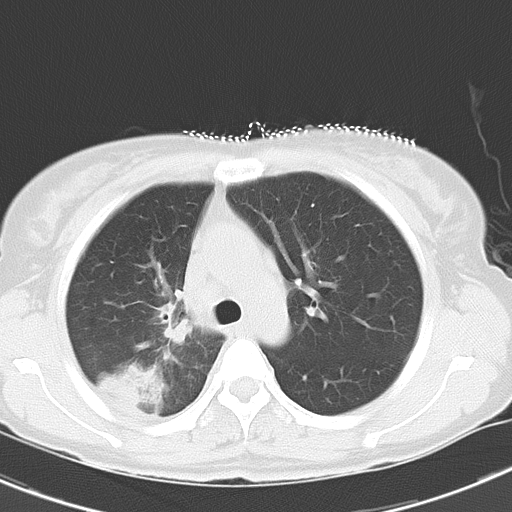
Chest CT, one axial slice. Position 21 of 29 along the scan axis. Reconstruction kernel B70f. 120 kVp. Lung window (W 1500 / L -600 HU). 512 × 512 image matrix, field of view 300 × 300 mm. Patient: female, 47 years. From the clinical record (not read from this slice): clinical TNM (as recorded): T1c N3 M0.
Outlined on this slice (rectangle marked by the reading radiologist):
- lung tumour (recorded histology: adenocarcinoma): bounding box (x1, y1, x2, y2) in pixels: (92, 353, 166, 412)